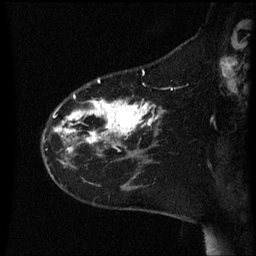
Breast MRI (dynamic contrast-enhanced), one sagittal slice. Position 16 of 60 along the scan axis. Dynamic contrast-enhanced series, image 2 of 3 at this slice position (ordered by acquisition). 1.5 T. TE 4.2 ms, TR 8.4 ms. 2.2 mm slice thickness. 256 × 256 image matrix, field of view 200 × 200 mm. Patient: female, 35 years. From the clinical record (not read from this slice): setting: breast cancer imaged before/during neoadjuvant chemotherapy; receptor status: HER2-positive.
Annotated regions visible in this slice (semi-automatic segmentation, software-assisted and operator-edited):
- analysis volume of interest (the breast-tissue region the enhancement analysis was run in; not a lesion): bounding box <43,78,167,163> (left, top, right, bottom; pixels)
- tumour enhancement mask (voxels above the 70 % enhancement threshold inside the analysis volume of interest): <55,96,163,151>